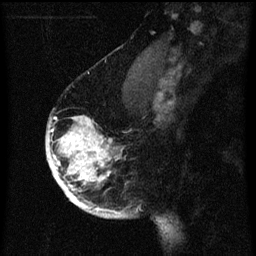
Breast MRI (dynamic contrast-enhanced), one sagittal slice; slice 45 of 60 in the series (ordered by position); dynamic contrast-enhanced series, image 2 of 3 at this slice position (ordered by acquisition); 1.5 T; TE 4.2 ms, TR 8 ms; 2 mm slice thickness; 256 × 256 image matrix, field of view 180 × 180 mm. Patient: female, 56 years.
Annotated regions visible in this slice (semi-automatically segmented with operator editing):
- analysis volume of interest (the breast-tissue region the enhancement analysis was run in; not a lesion): bounding box (x1, y1, x2, y2) in pixels: (46, 112, 125, 219)
- tumour enhancement mask (voxels above the 70 % enhancement threshold inside the analysis volume of interest): (46, 116, 125, 219)